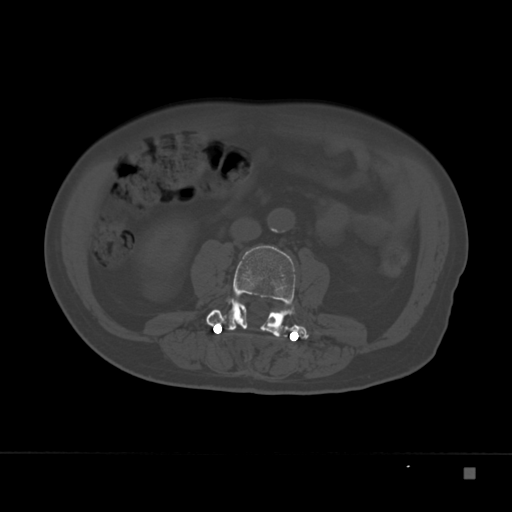
CT including the spine, one axial slice. Position 65 of 332 along the scan axis. Reconstruction kernel Br40s. 120 kVp. Bone window (W 1800 / L 400 HU). 1.5 mm slice thickness. 512 × 512 image matrix, field of view 389 × 389 mm. Male patient, age 72 years. From the clinical record (not read from this slice): primary cancer: skeletal.
Outlined on this slice (semi-automatic segmentation, software-assisted and operator-edited):
- L3 vertebra: bounding box (x1, y1, x2, y2) in pixels: (206, 245, 309, 342)